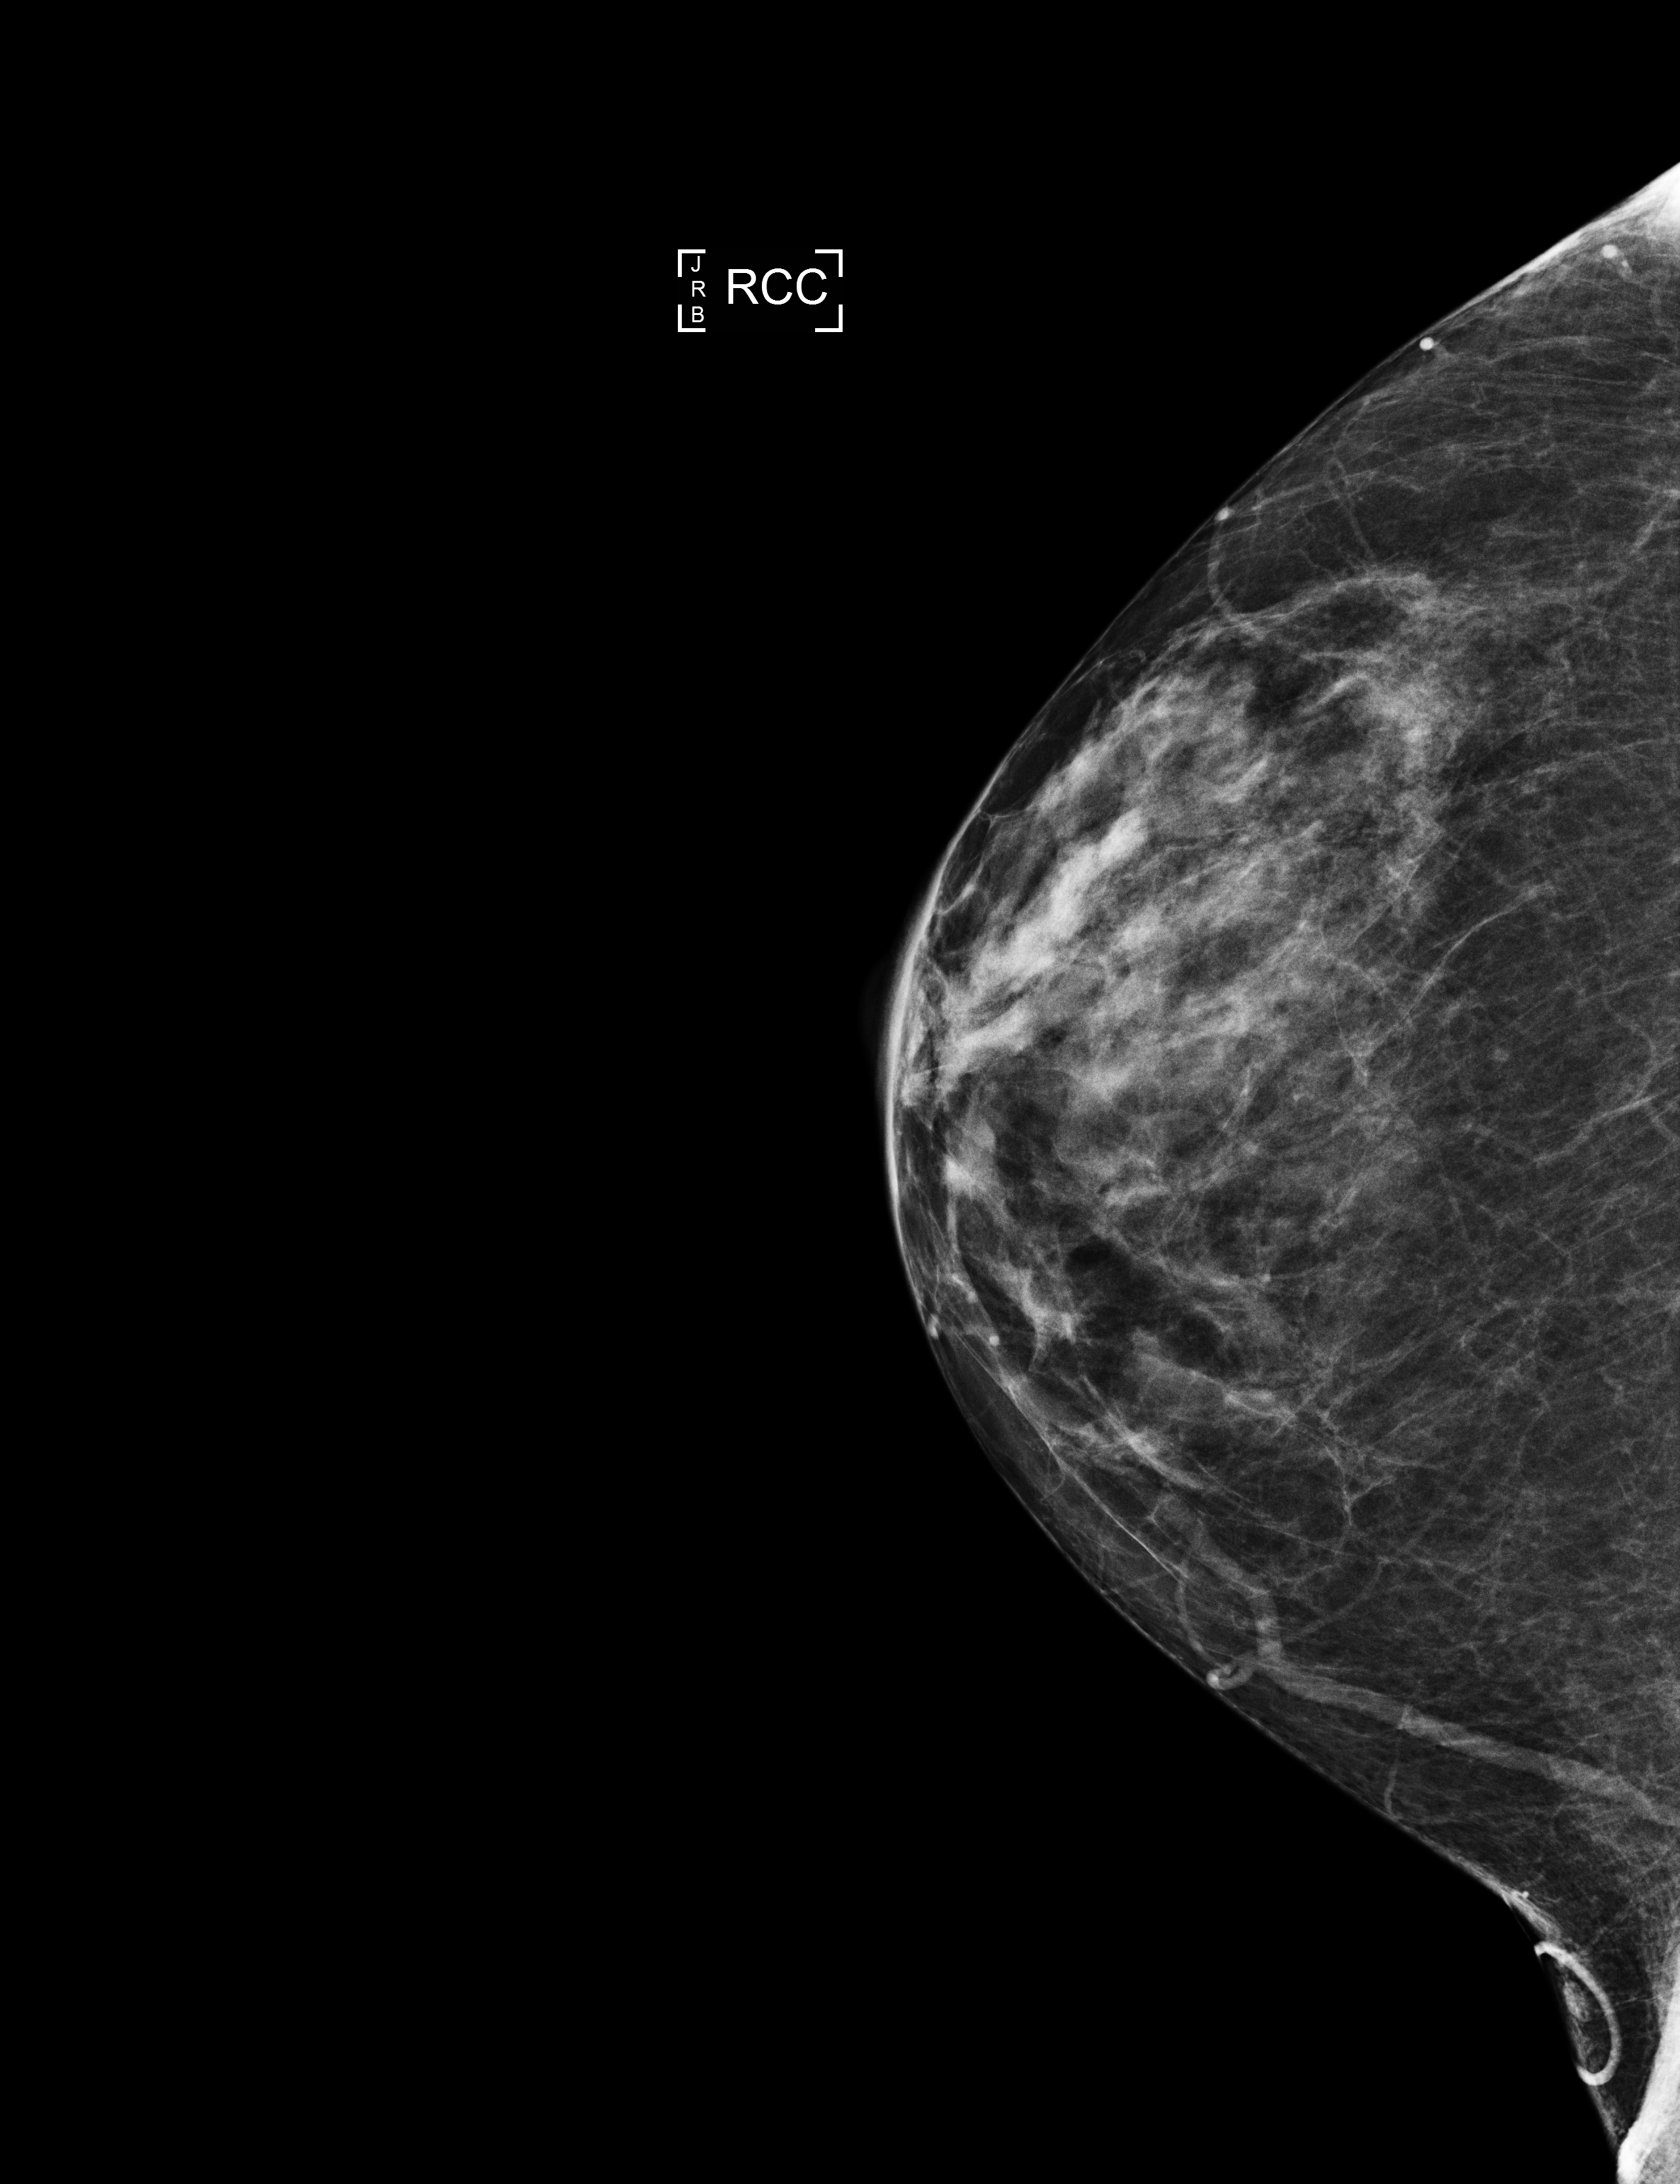
Annual screening mammography examination; compressed breast thickness 41 mm. Patient: female, 60 years.
Image type: full-field digital mammogram. Breast: right. Projection: craniocaudal (CC) view.